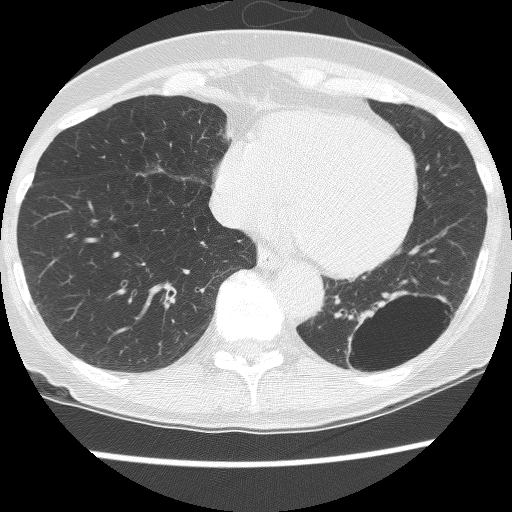
Chest CT (low-dose screening protocol), one axial image; third screening round (two years after baseline); lung window (W 1500 / L -600 HU); 2.5 mm slice thickness; lung (sharp) reconstruction kernel (BONE); slice 91 of 130 in the series; 512 × 512 image matrix, field of view 290 × 290 mm. Female participant, aged 61 years at enrolment. Current smoker at enrolment.
Lesion marked by an expert reader, bounding box (x1, y1, x2, y2) in pixels: (332, 292, 445, 388). The screening reader recorded 2 non-calcified nodules or masses ≥4 mm on this exam; which of them this box marks is not recorded. Official screen result: positive, no significant change: stable abnormalities potentially related to lung cancer, unchanged since the prior screening exam. Lung cancer was diagnosed 166 days after this screen: non-small cell carcinoma, left lower lobe, poorly differentiated (G3), stage IB (AJCC 6th edition), 100 mm at pathology.